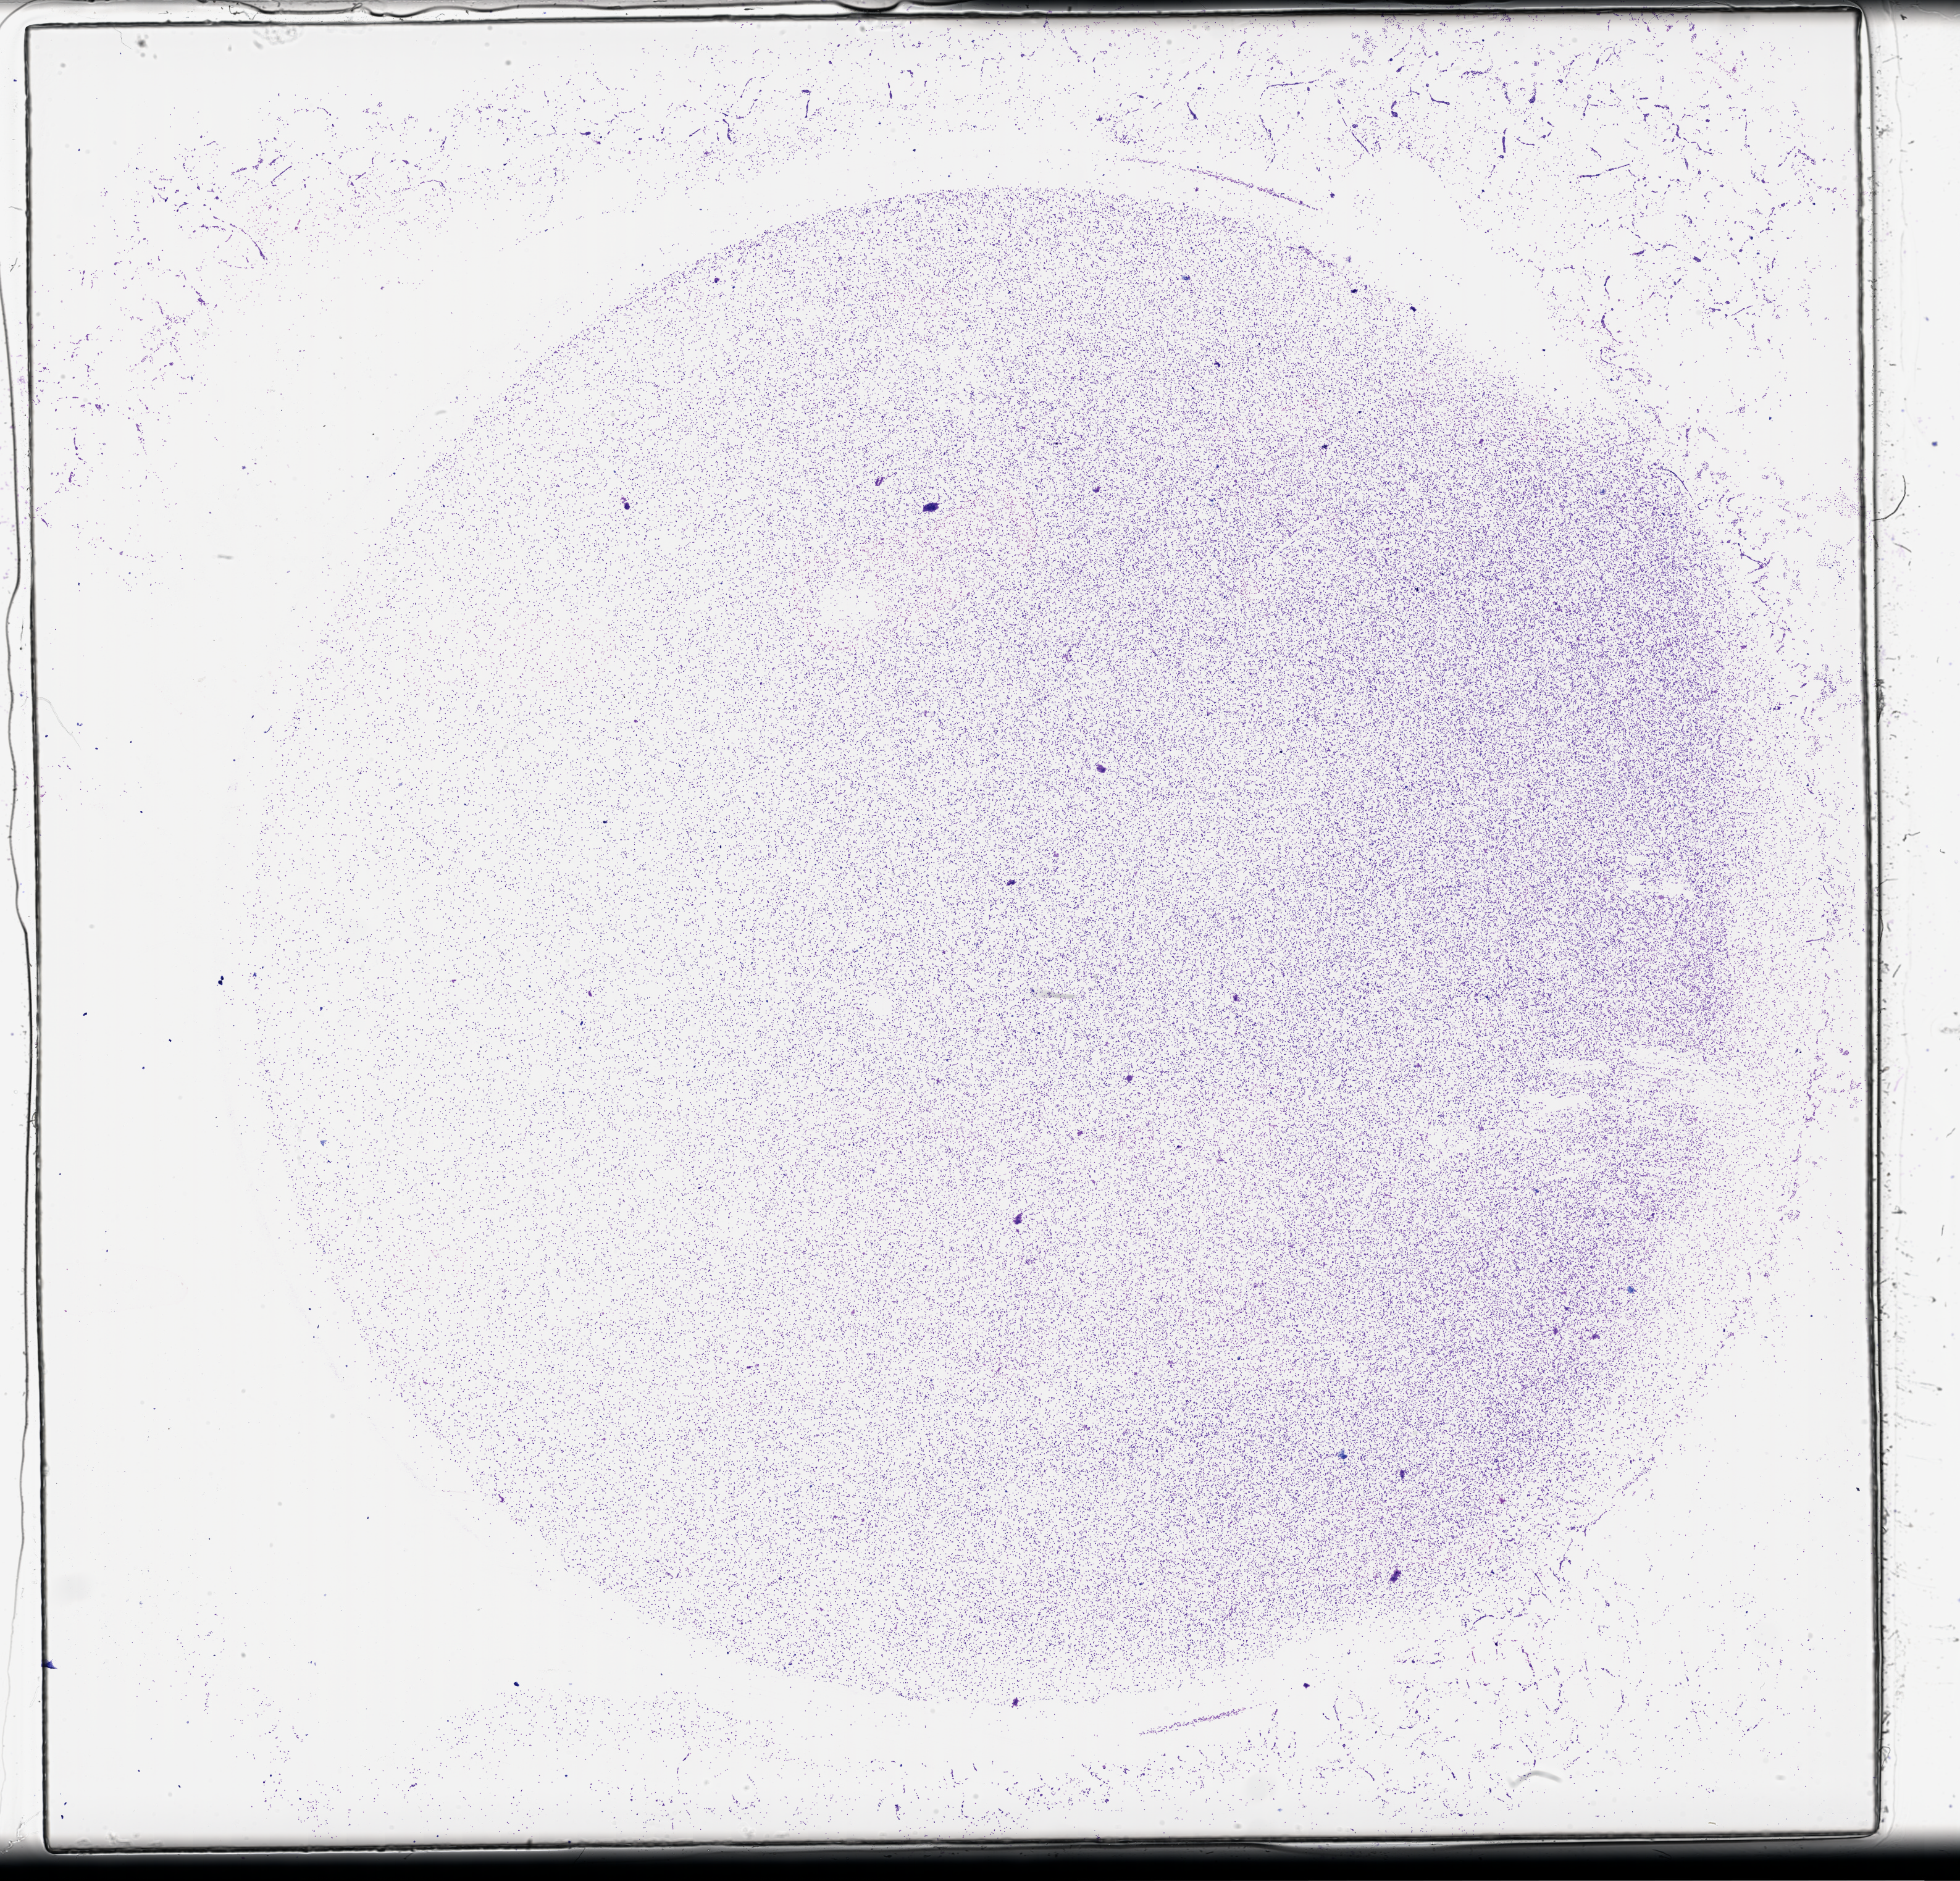
Whole-slide histology image, Hematoxylin and eosin (H&E) stained — whole scanned area (about 25.6 x 24.6 mm) shown as a low-resolution overview; bone marrow (leukaemic) sample. 49-year-old female patient. Blasts: 90%.
Diagnosis: Acute Myeloid Leukemia. FAB classification: M1. WHO classification: AML without maturation.